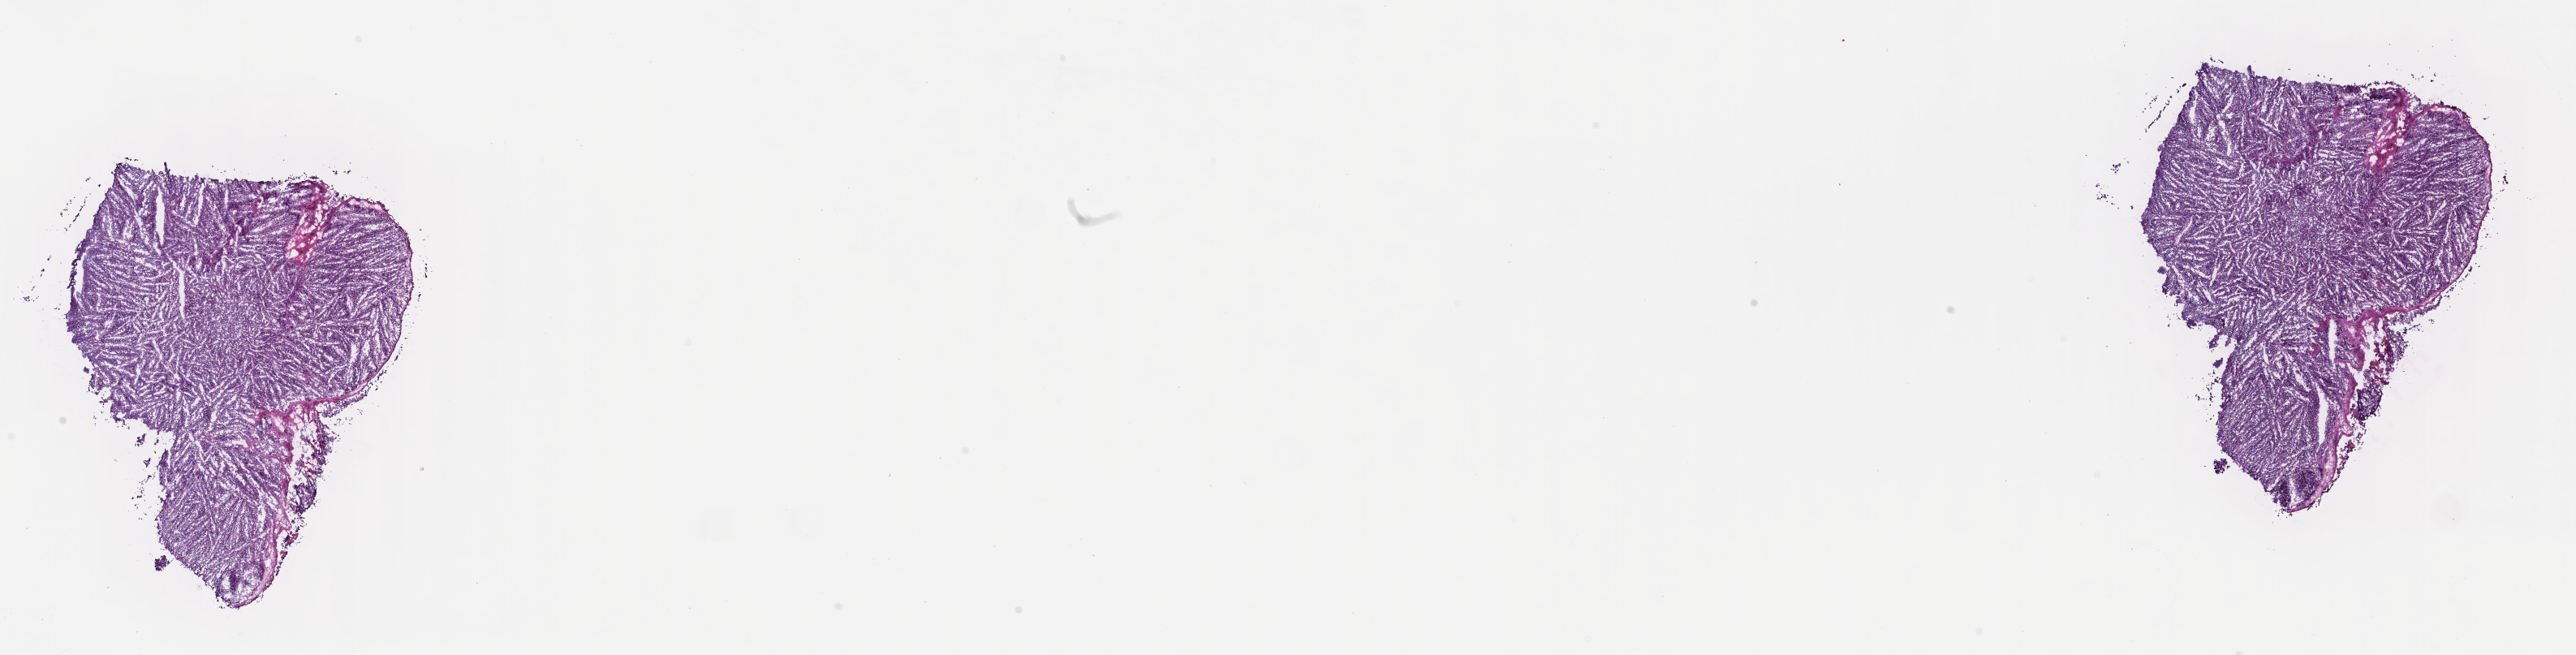
Whole-slide image, haematoxylin and eosin stain — shown as a low-resolution overview of the whole scanned area (about 25.7 x 6.5 mm), cryosection, primary tumor, anatomic site: lymph node of head and neck. Female, age 8 years at initial diagnosis. Slide review estimates, as recorded: tumor cells 95%, tumor nuclei 95%, stromal cells 5%, necrosis 0%, normal cells 0%. Infiltration values recorded for this section: lymphocyte infiltration 10%, monocyte infiltration 20%, neutrophil infiltration 10%.
Diagnosis: Burkitt lymphoma, NOS.